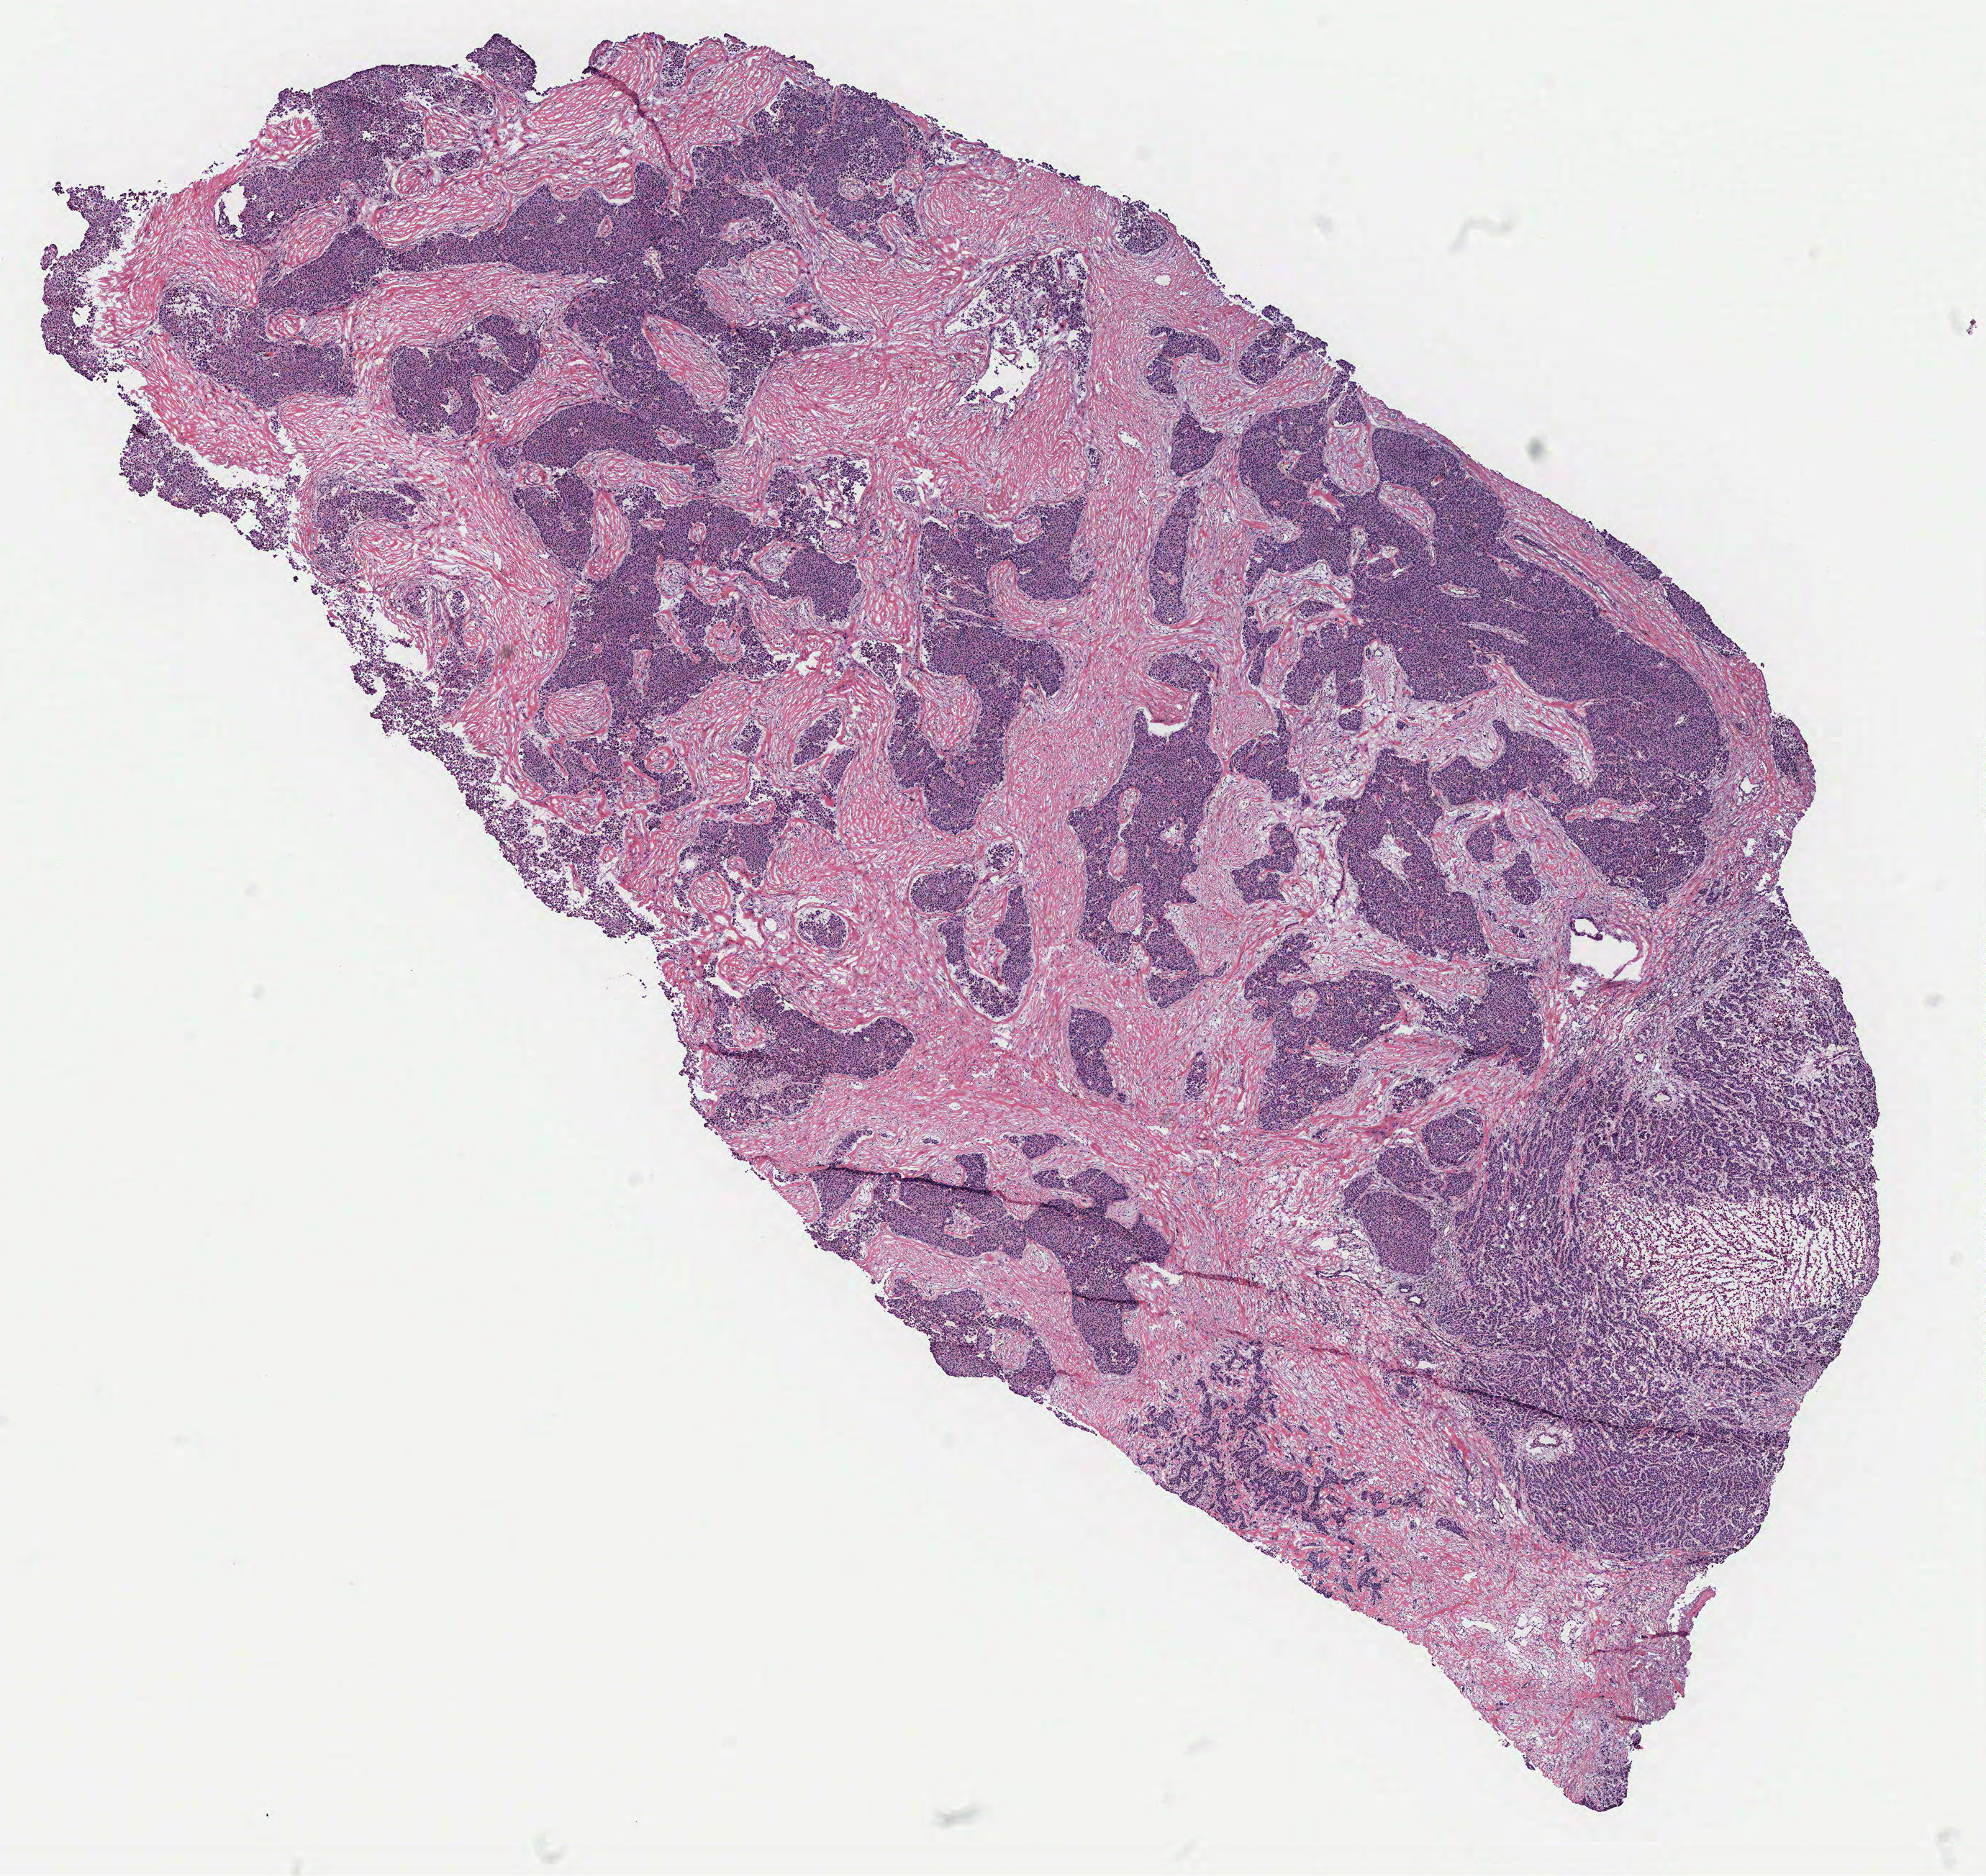
H&E-stained whole-slide image — a low-resolution overview of the entire scanned area, about 11.0 x 10.4 mm, breast, tissue type not recorded. 78-year-old female patient.
Patient diagnosis: Infiltrating duct carcinoma, NOS.